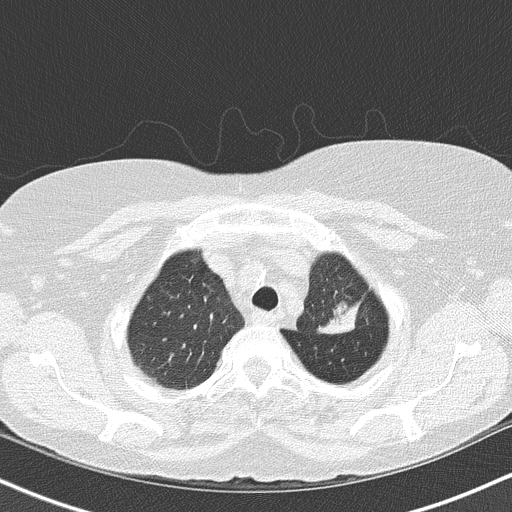
Axial slice from a low-dose chest CT screening exam; third screening round (two years after baseline); lung window (W 1500 / L -600 HU); 2 mm slice thickness; lung (sharp) reconstruction kernel (B50f); slice 127 of 147 in the series. Female participant, aged 68 years at enrolment. Former smoker at enrolment.
- Expert-annotated lung lesion, bounding box <287,239,379,345> (left, top, right, bottom; pixels).
- Reader record for this screening exam (exam-level; its link to the box is not recorded): non-calcified nodule or mass ≥4 mm, left upper lobe, 5 × 5 mm, poorly defined margins, mixed attenuation, pre-existing on the prior screen: yes; interval growth: yes.
- Official screen result: positive, other.